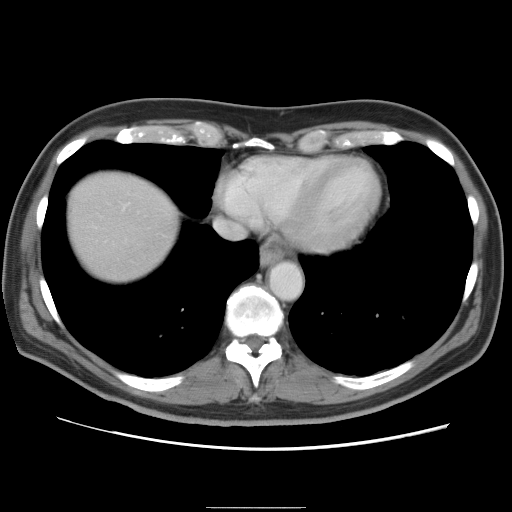
Contrast-enhanced abdominal CT, one axial slice; position 78 of 87 along the scan axis; intravenous contrast given; soft-tissue window (W 400 / L 40 HU); 512 × 512 image matrix. Male patient, age 63 years. Case-level facts recorded for this patient, not image findings: diagnosis: colorectal cancer liver metastases, imaged before liver resection; multiple liver metastases: no; largest metastasis: 9 cm; disease in both lobes: no.
Annotated regions visible in this slice (outlined manually by an expert reader):
- liver: bounding box (x1, y1, x2, y2) in pixels: (68, 173, 177, 281)
- planned liver remnant (the part of the liver to remain after resection): (68, 184, 177, 281)